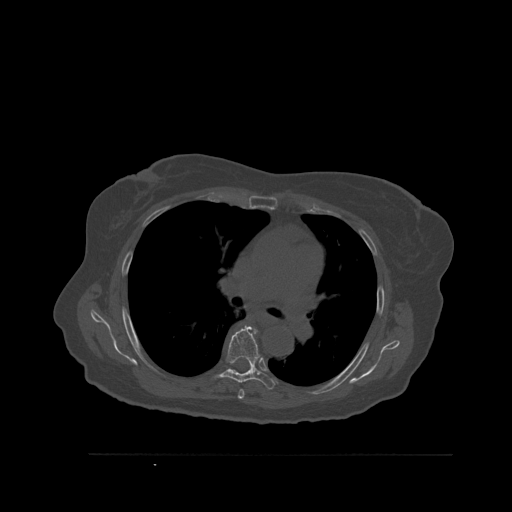
CT including the spine, one axial slice. Slice 382 of 527 in the series (ordered by position). Bone window (W 1800 / L 400 HU). 512 × 512 image matrix, field of view 470 × 470 mm. Female patient, age 73 years. From the clinical record (not read from this slice): primary cancer: breast.
Outlined on this slice (semi-automatically segmented with operator editing):
- T5 vertebra: bounding box (x1, y1, x2, y2) in pixels: (238, 390, 245, 399)
- T6 vertebra: (216, 326, 275, 390)